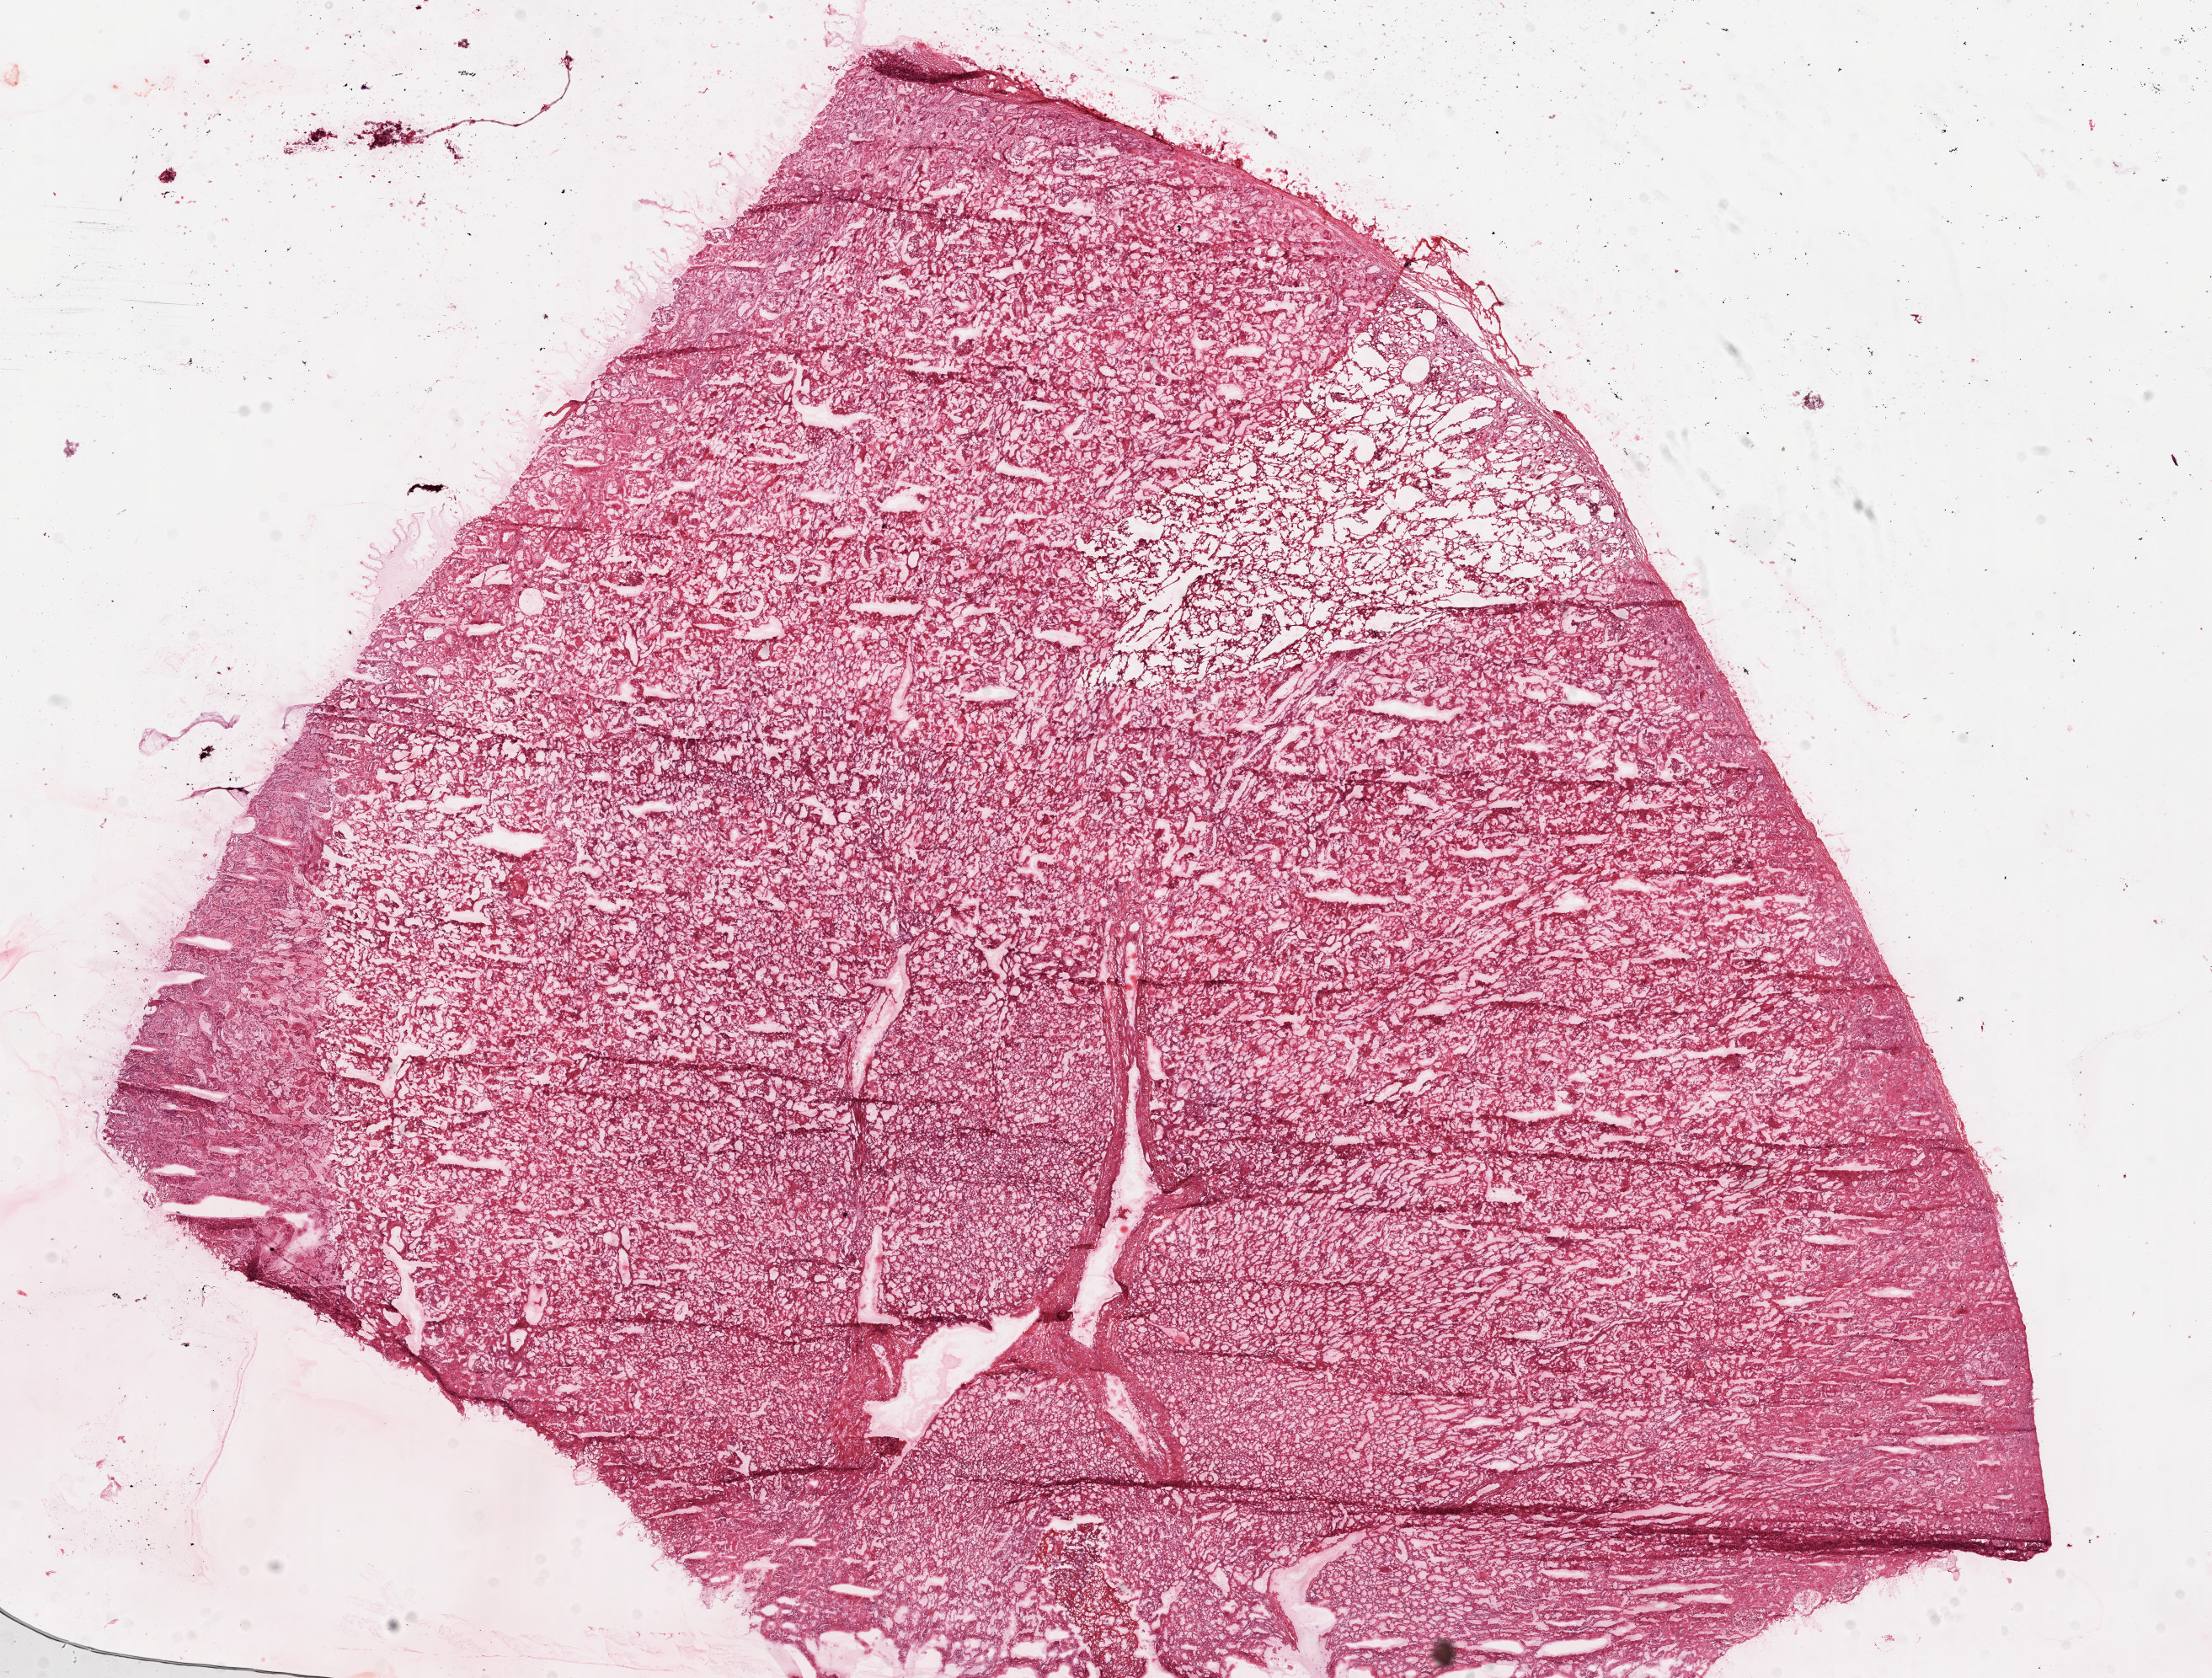
Hematoxylin and eosin (H&E) stained whole-slide image, shown as a low-resolution overview of the whole scanned area (about 20.8 x 15.8 mm, slide scanned at 20x); frozen section from the top of the tissue portion; kidney, solid tissue normal (non-tumour tissue) sample. Male, age 51 years at initial diagnosis.
This section: solid tissue normal (non-tumour) sample from the same patient. Patient diagnosis: Clear cell adenocarcinoma, NOS.